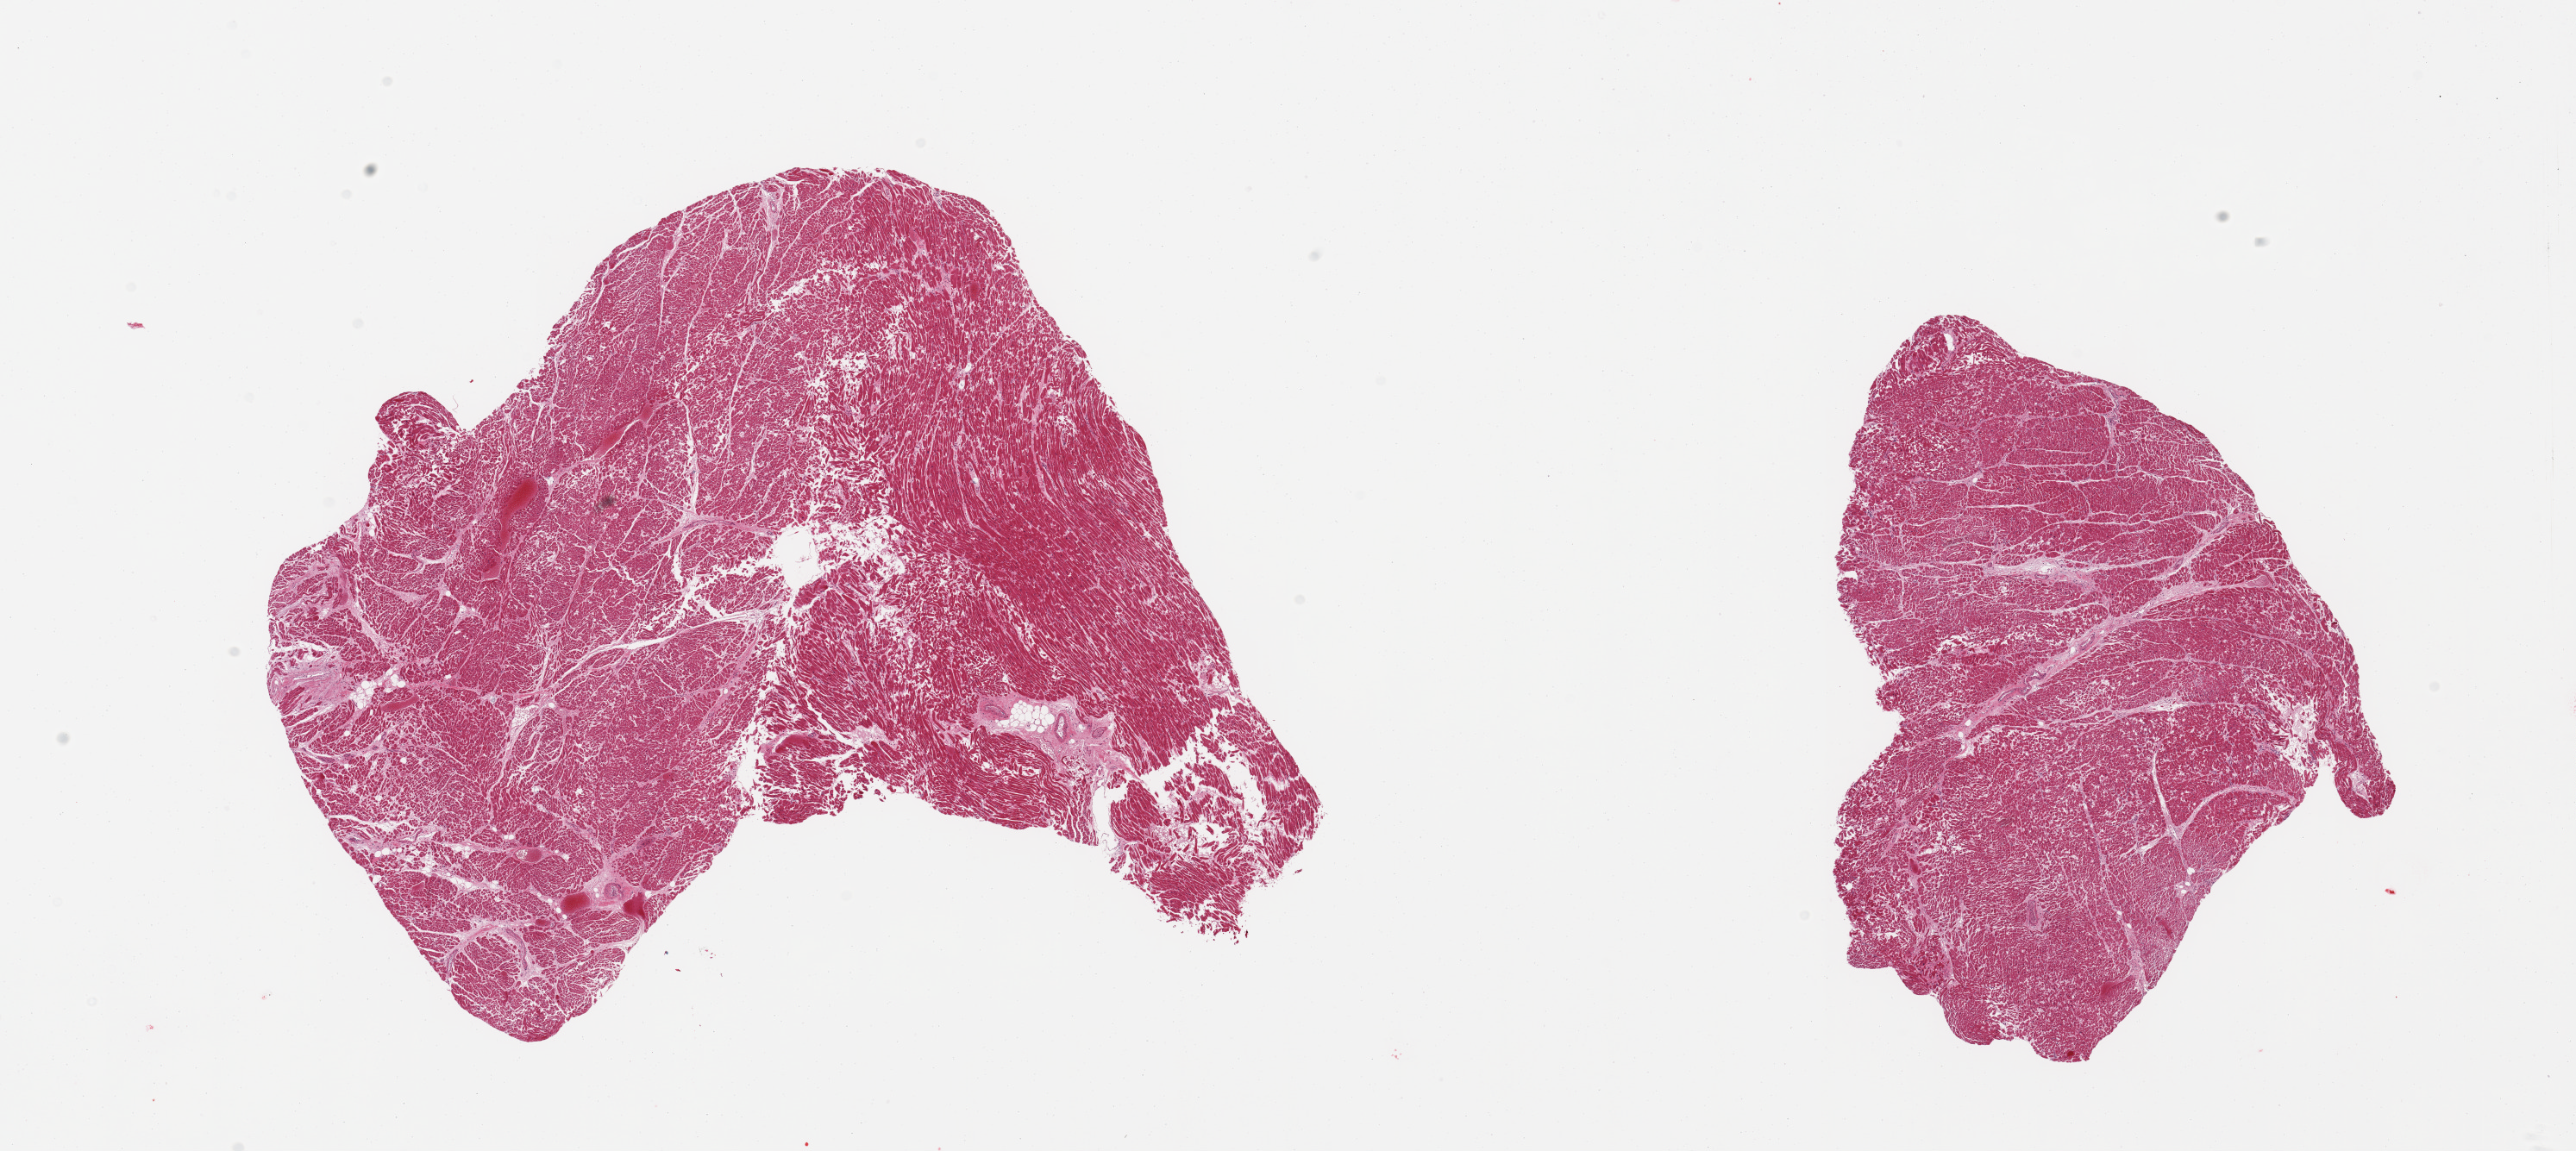
H&E whole-slide image, a low-resolution overview of the entire scanned area, about 23.6 x 10.6 mm. PAXgene-fixed, paraffin-embedded tissue. Sampled site (target tissue): heart. Tissue donor sample. Donor: female.
Reviewer comment on this tissue sample: 2 pieces; accentuation of interstitial connective tissue; congestion.